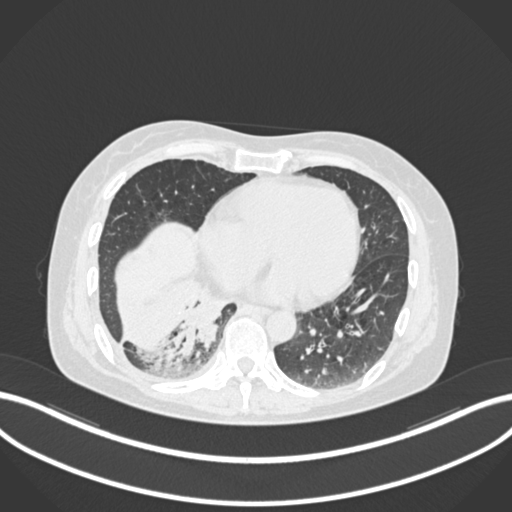
Chest CT, one axial slice; slice 49 of 168 in the series (ordered by position); reconstruction kernel B30f; 120 kVp; lung window (W 1500 / L -600 HU); 512 × 512 image matrix, field of view 400 × 400 mm. Patient: female, 63 years. From the clinical record (not read from this slice): clinical TNM (as recorded): T1c N0 M0.
Structures marked on this image (bounding box drawn by a radiologist):
- lung tumour (recorded histology: adenocarcinoma): box from (x=171, y=292) to (x=229, y=360) px